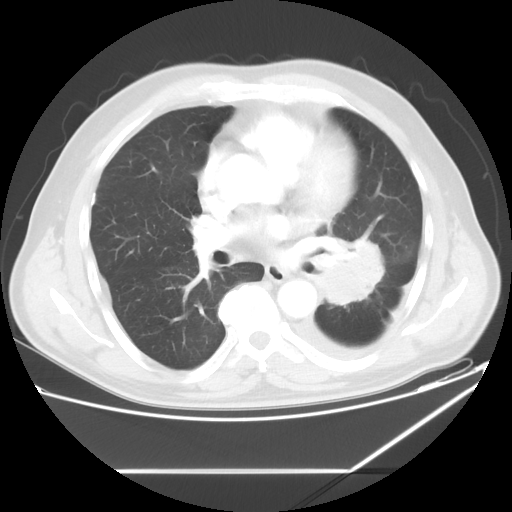
Chest CT, one axial slice. Slice 31 of 60 in the series (ordered by position). Reconstruction kernel STANDARD. Lung window (W 1500 / L -600 HU). 512 × 512 image matrix. Male patient, age 62 years. Case-level facts recorded for this patient, not image findings: clinical TNM (as recorded): T3 N0 M1.
Structures marked on this image (bounding box drawn by a radiologist):
- lung tumour (recorded histology: adenocarcinoma): box from (x=311, y=233) to (x=389, y=305) px
- lung tumour (recorded histology: adenocarcinoma): (x=312, y=231)–(x=389, y=309)